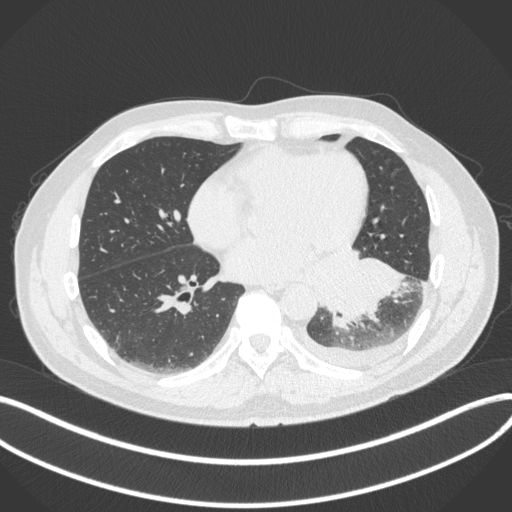
Chest CT, one axial slice. Position 146 of 350 along the scan axis. Reconstruction kernel B31f. Lung window (W 1500 / L -600 HU). 512 × 512 image matrix, field of view 400 × 400 mm. Patient: male, 58 years. Case-level facts recorded for this patient, not image findings: clinical TNM (as recorded): T3 N1 M1b.
Outlined on this slice (rectangle marked by the reading radiologist):
- lung tumour (recorded histology: small cell carcinoma): bounding box (x1, y1, x2, y2) in pixels: (328, 254, 405, 331)